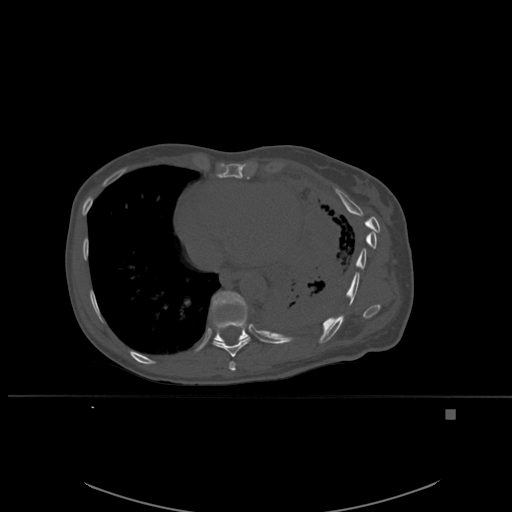
CT including the spine, one axial slice. Slice 329 of 537 in the series (ordered by position). Bone window (W 1800 / L 400 HU). 1.5 mm slice thickness. 512 × 512 image matrix, field of view 440 × 440 mm. Patient: female, 45 years. From the clinical record (not read from this slice): primary cancer: lung.
Outlined on this slice (semi-automatic segmentation, software-assisted and operator-edited):
- T10 vertebra: bounding box <211,291,250,342> (left, top, right, bottom; pixels)
- T8 vertebra: <229,361,236,371>
- T9 vertebra: <210,302,250,357>